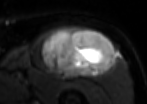
MRI of an extremity soft-tissue mass, one axial slice; slice 61 of 85 in the series (ordered by position); T2-weighted fat-saturated; MR volume resampled by the dataset authors to the PET/CT grid (not the native acquisition matrix); 3.27 mm slice thickness; 147 × 104 image matrix. Male patient. From the clinical record (not read from this slice): histological type: extraskeletal osteosarcoma; grade: high; site of the primary tumour: thigh.
Structures marked on this image (expert contour drawn on MRI and transferred to this co-registered scan by the dataset authors):
- gross tumour volume (mass): box from (x=40, y=26) to (x=116, y=79) px